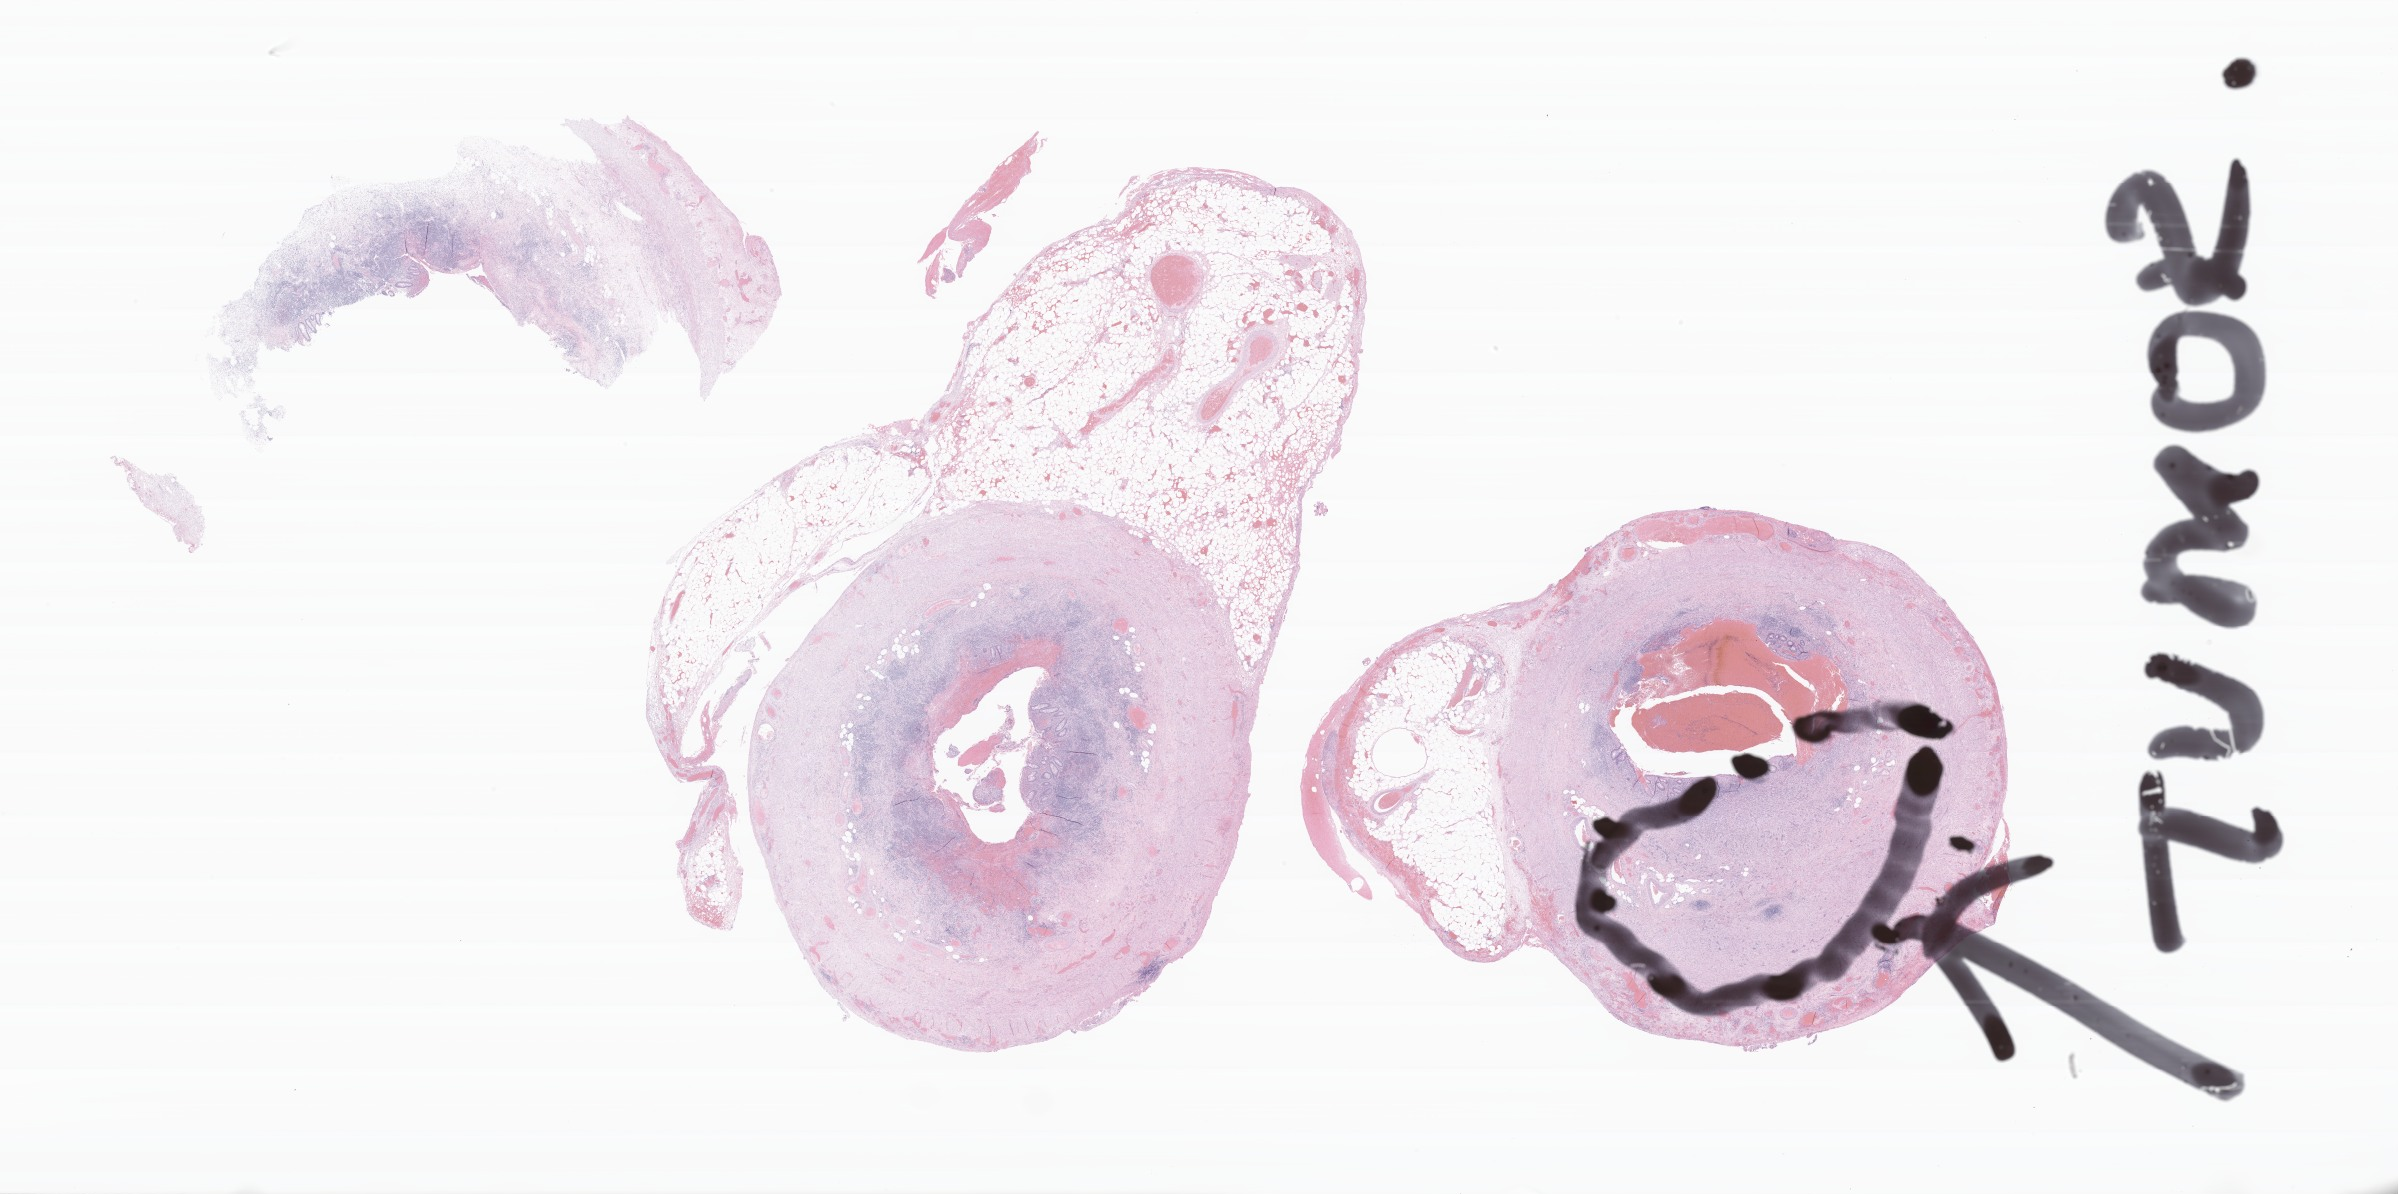
Whole-slide image, hematoxylin and eosin (H&E) stain of tumor tissue from the appendix — shown as a low-resolution overview of the whole scanned area (about 40.3 x 20.1 mm); FFPE section. Patient female; age 206 months (17 years 2 months).
* diagnosis: Neuroendocrine carcinoma, NOS